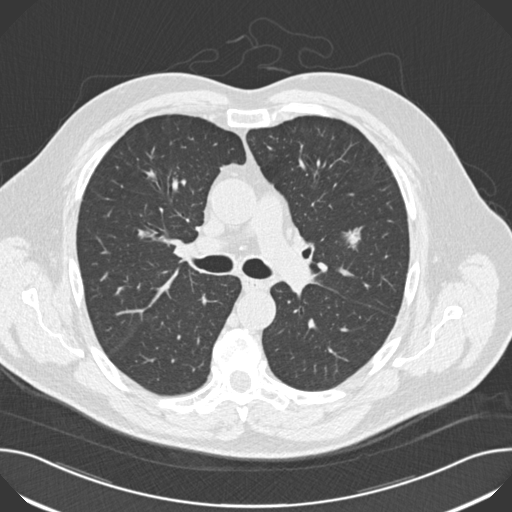
Low-dose screening chest CT, one axial slice; slice 109 of 174 in the series (ordered by position); reconstruction kernel B30f; lung window (W 1500 / L -600 HU); 512 × 512 image matrix.
Annotated regions visible in this slice (expert manual segmentation):
- lesion 1 (tumor, upper lobe of left lung): box from (x=346, y=227) to (x=362, y=248) px